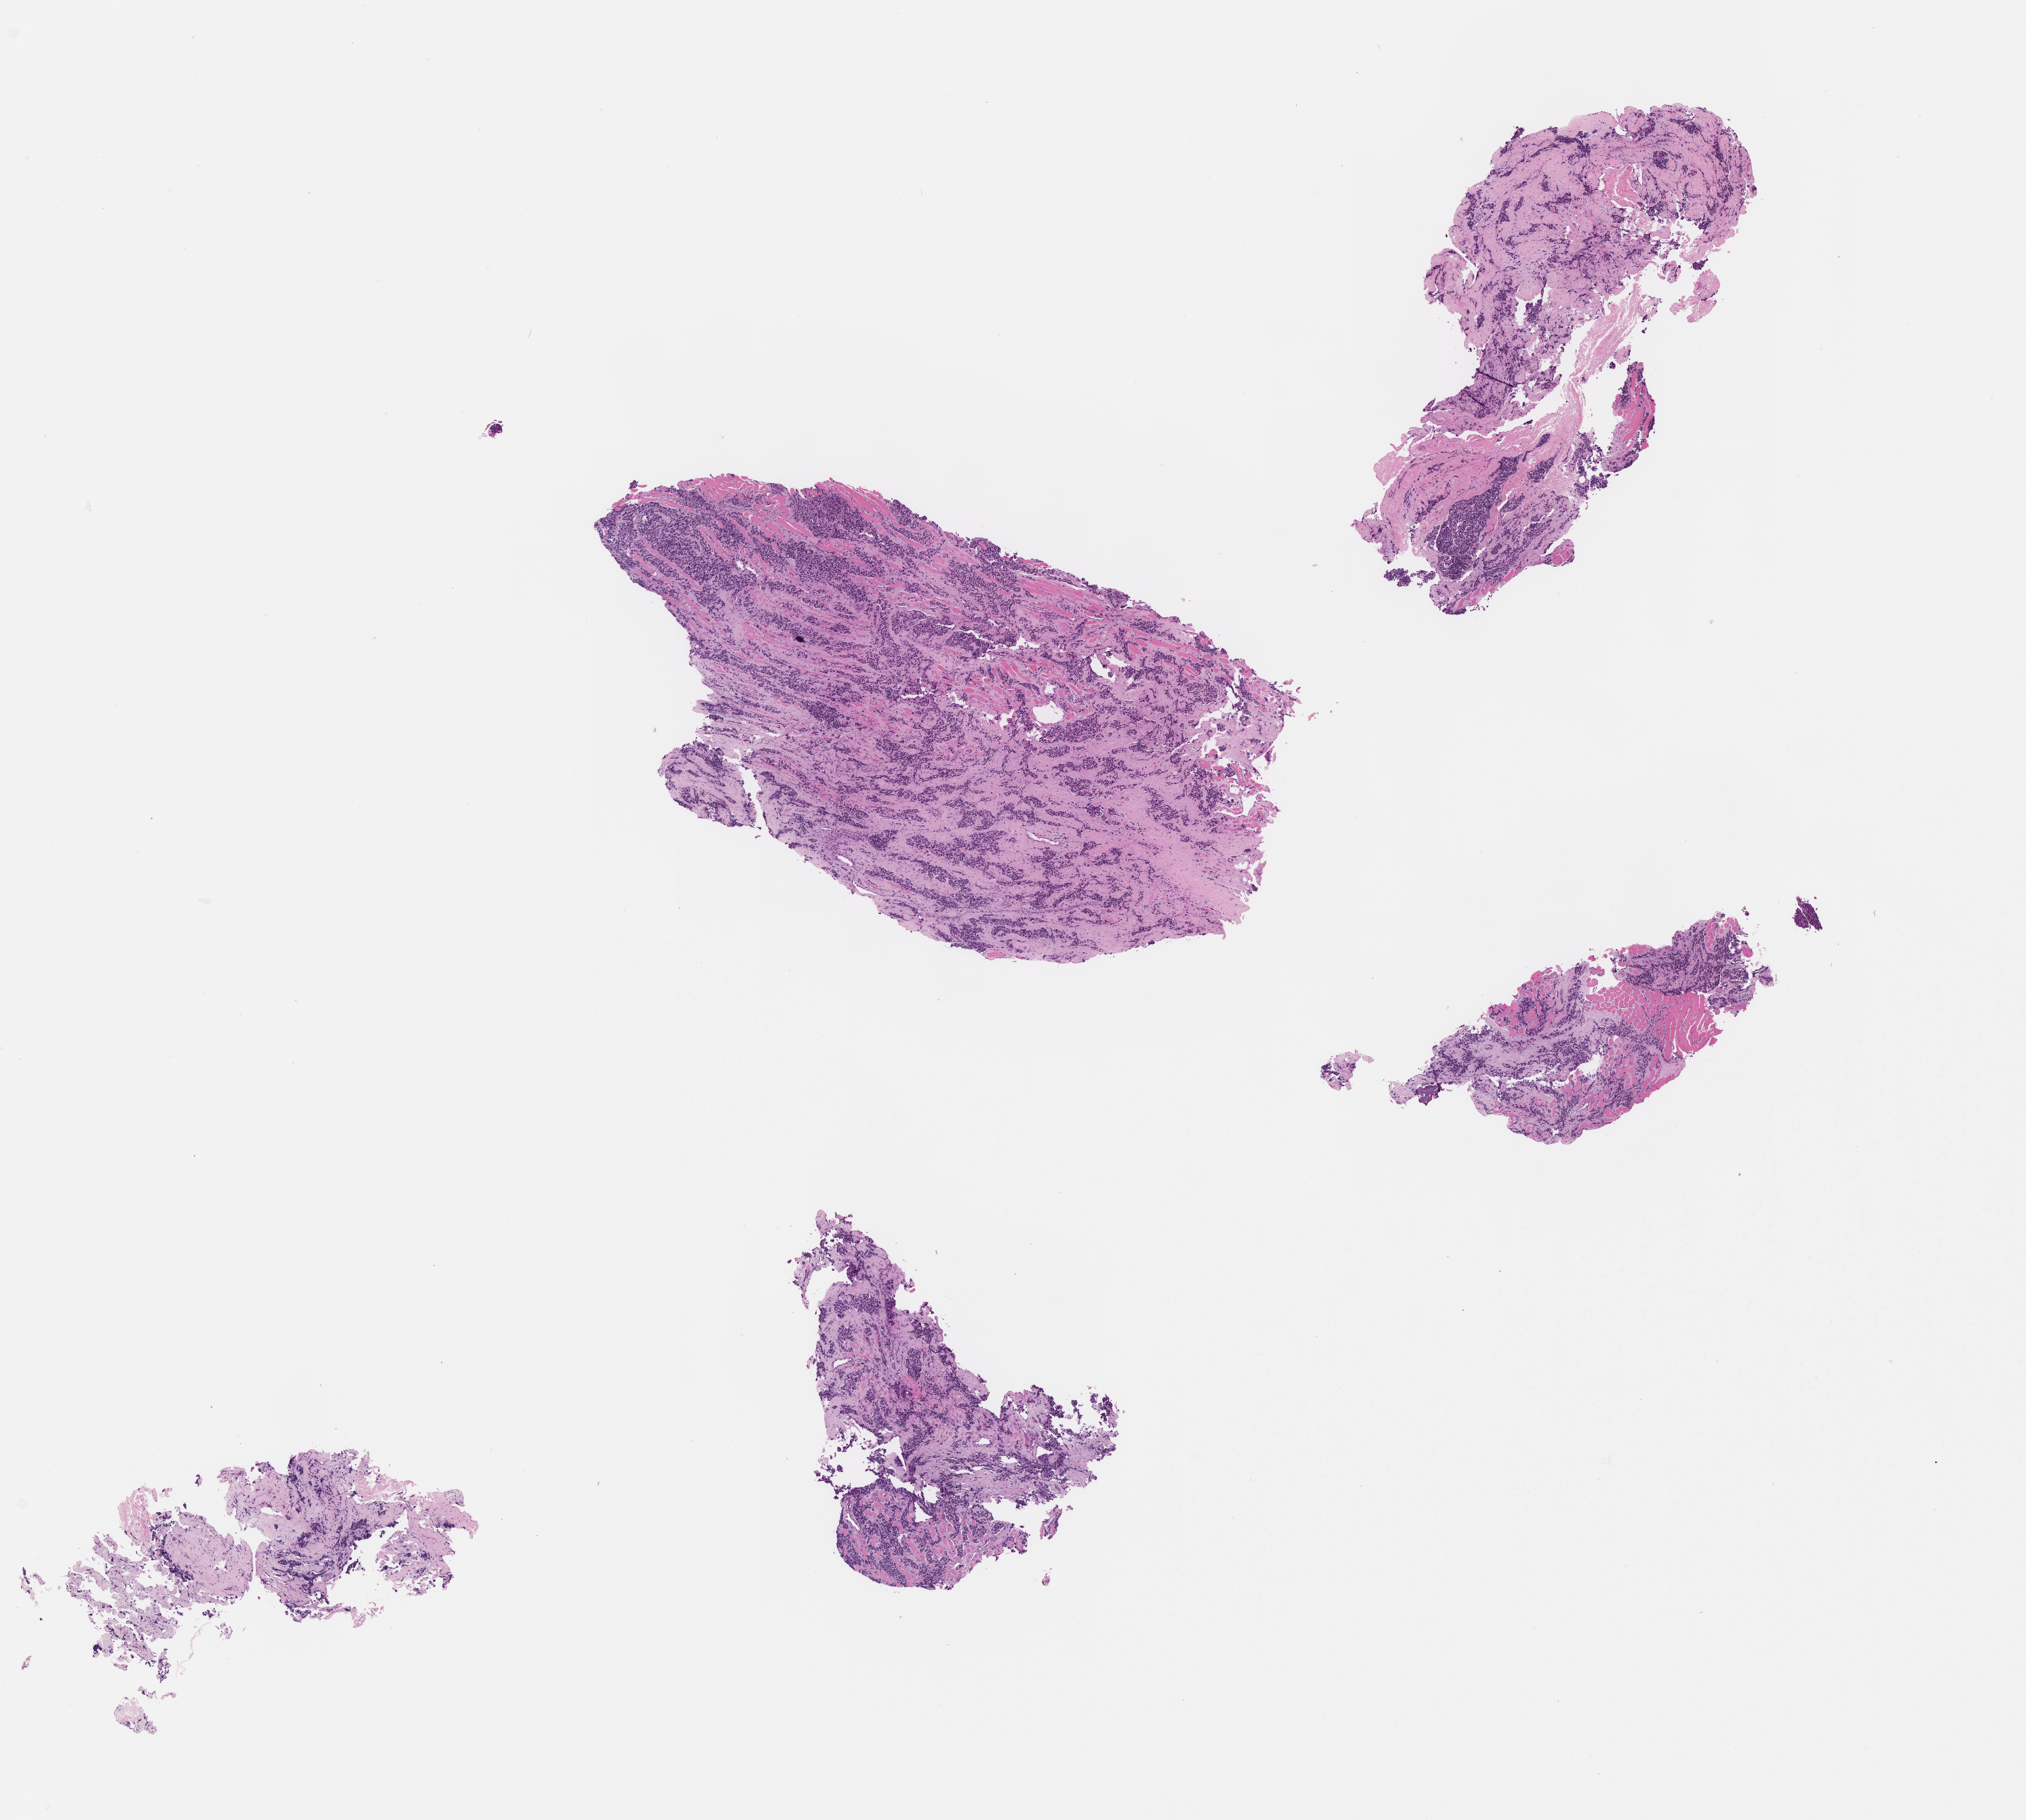
Digitized hematoxylin and eosin (H&E)-stained section of tumor tissue, a low-resolution overview of the entire scanned area, about 12.1 x 10.9 mm, FFPE section, site: foot. Patient: male, age 5.0 years at diagnosis.
Diagnosis: rhabdomyosarcoma; histological classification: alveolar rhabdomyosarcoma.